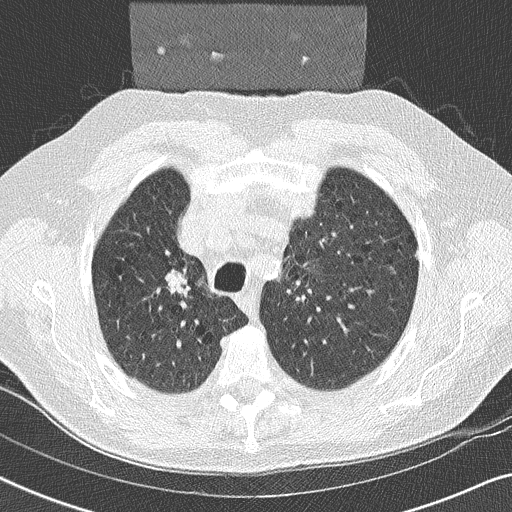
Low-dose screening chest CT, one axial slice. Slice 184 of 252 in the series (ordered by position). Lung window (W 1500 / L -600 HU). 2 mm slice thickness. 512 × 512 image matrix.
Structures marked on this image (manually delineated by an expert):
- lesion 1 (tumor, upper lobe of right lung): bounding box <165,270,186,292> (left, top, right, bottom; pixels)